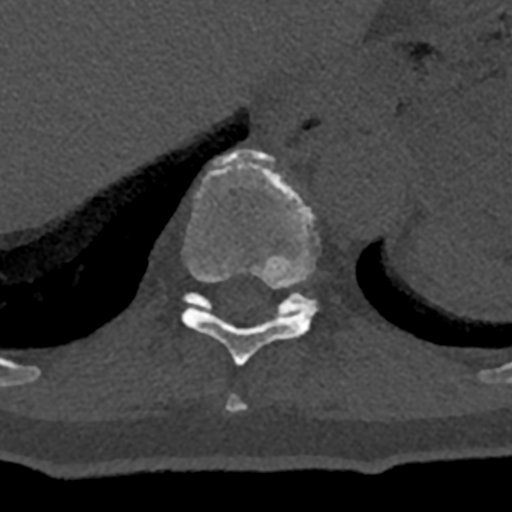
CT including the spine, one axial slice. Position 592 of 797 along the scan axis. 120 kVp. Bone window (W 1800 / L 400 HU). 0.5 mm slice thickness. 512 × 512 image matrix, field of view 160 × 160 mm. Male patient, age 74 years. Case-level facts recorded for this patient, not image findings: primary cancer: renal.
Annotated regions visible in this slice (semi-automatic segmentation, software-assisted and operator-edited):
- T10 vertebra: bounding box (x1, y1, x2, y2) in pixels: (182, 150, 319, 366)
- T11 vertebra: (183, 292, 316, 319)
- T9 vertebra: (225, 394, 246, 412)